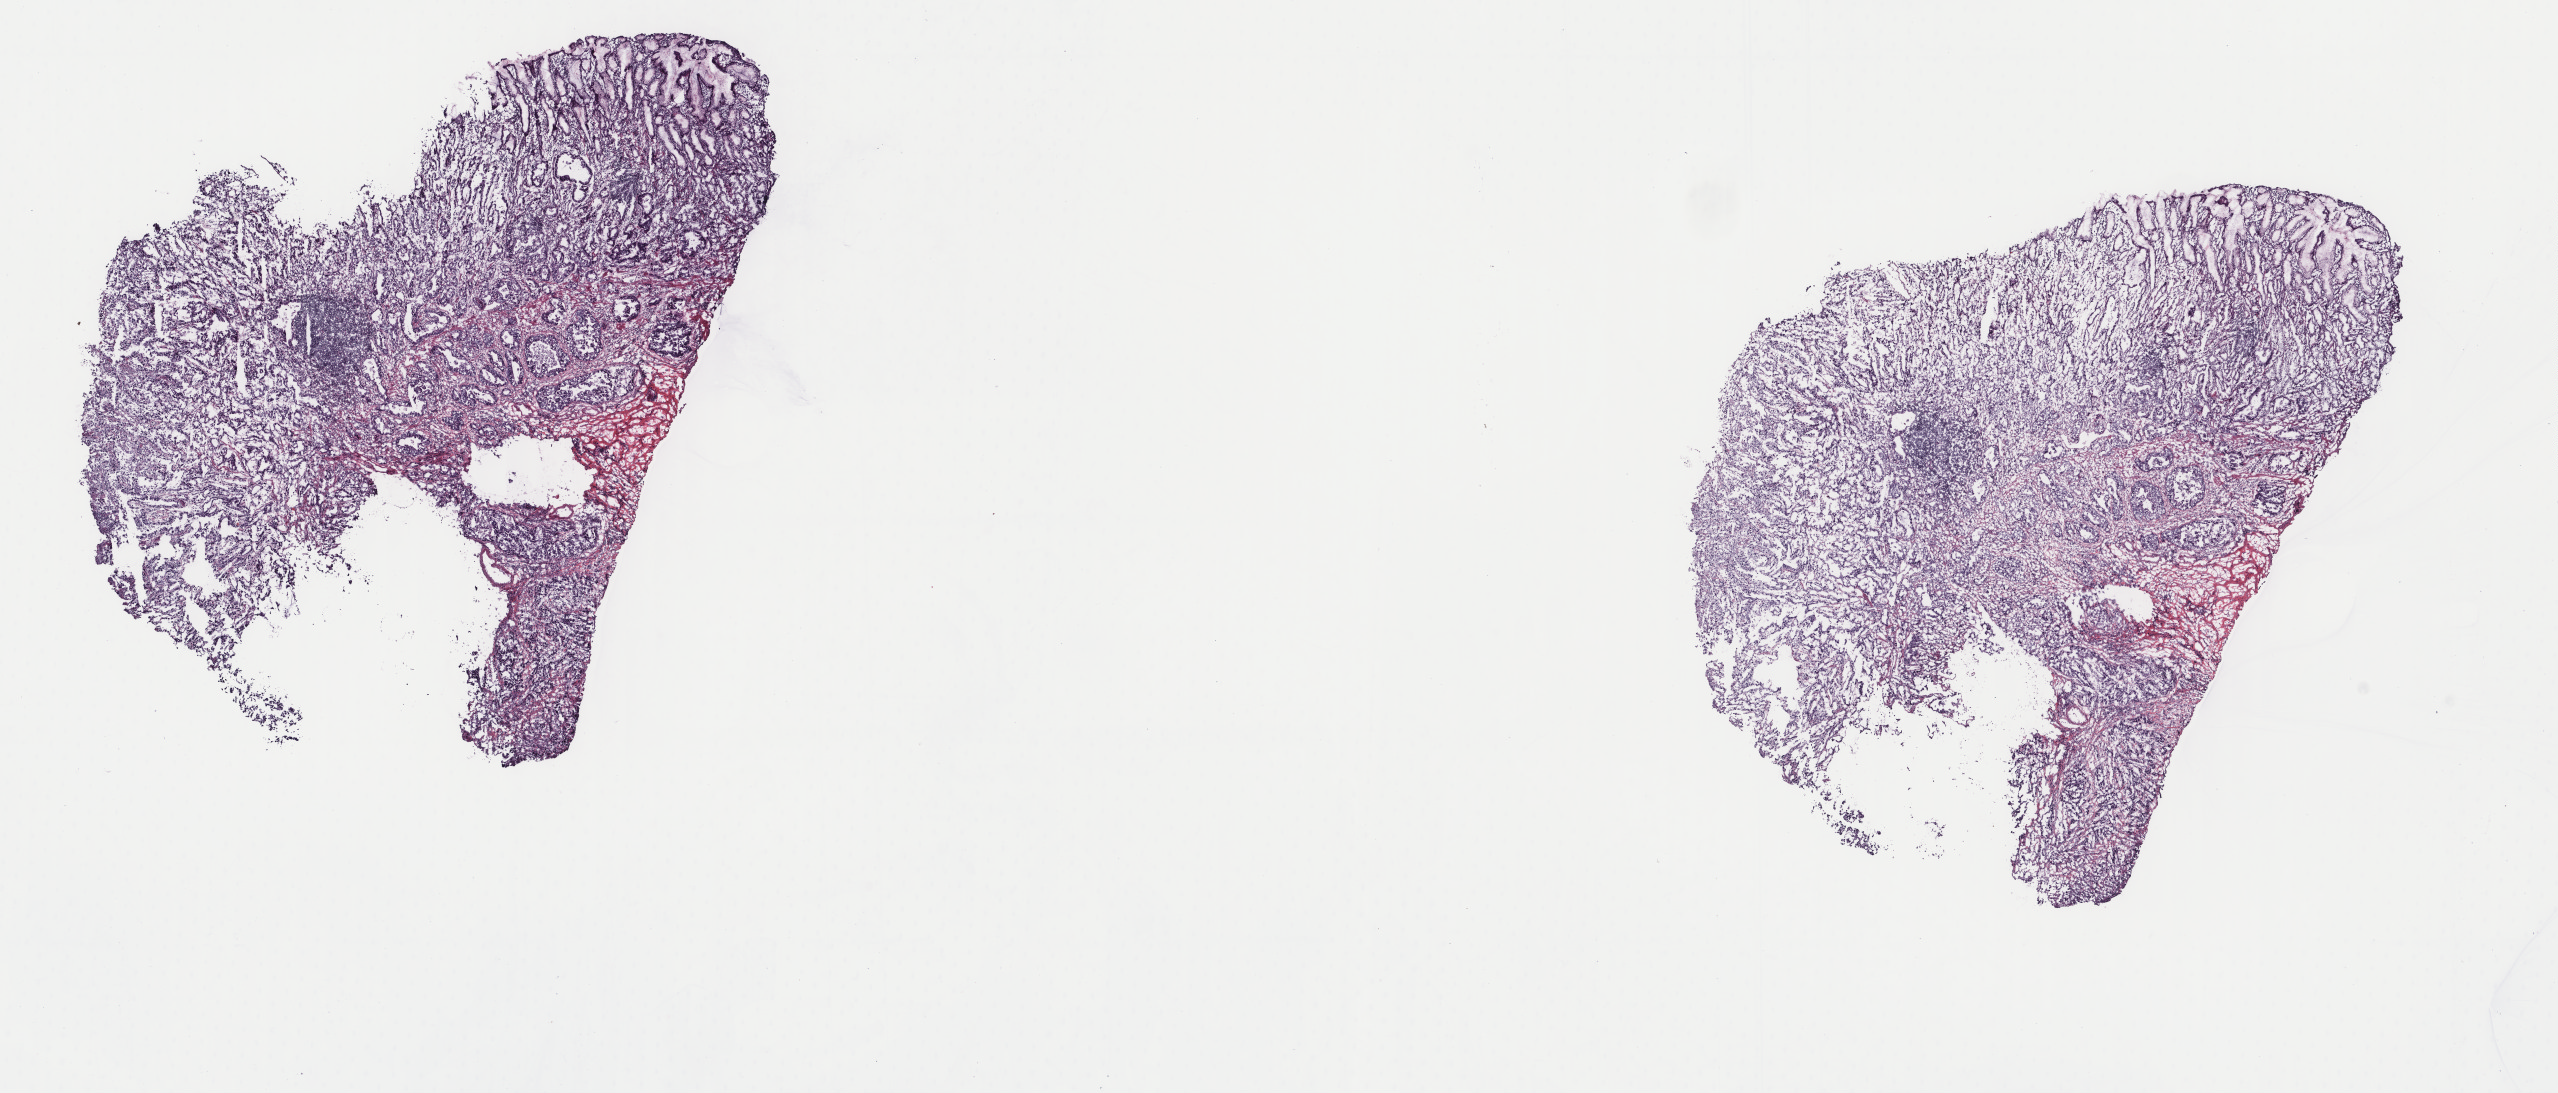
Digitized Hematoxylin and eosin (H&E) stained tissue section (whole slide), a low-resolution overview of the entire scanned area, about 20.3 x 8.7 mm. Frozen section. Primary tumour sample from the stomach. Female patient; age at initial diagnosis 58 years. Histologic grade: G2 (moderately differentiated). Slide review estimates, as recorded: tumour cells 43%, tumour nuclei 60%, normal cells 15%, stromal cells 30%, necrosis 12%. Inflammatory infiltration, as recorded: lymphocyte infiltration 15%, monocyte infiltration 0%, neutrophil infiltration 0%.
AJCC pathologic stage: IIIB (7th edition). Diagnosis: Tubular adenocarcinoma (gastric antrum).